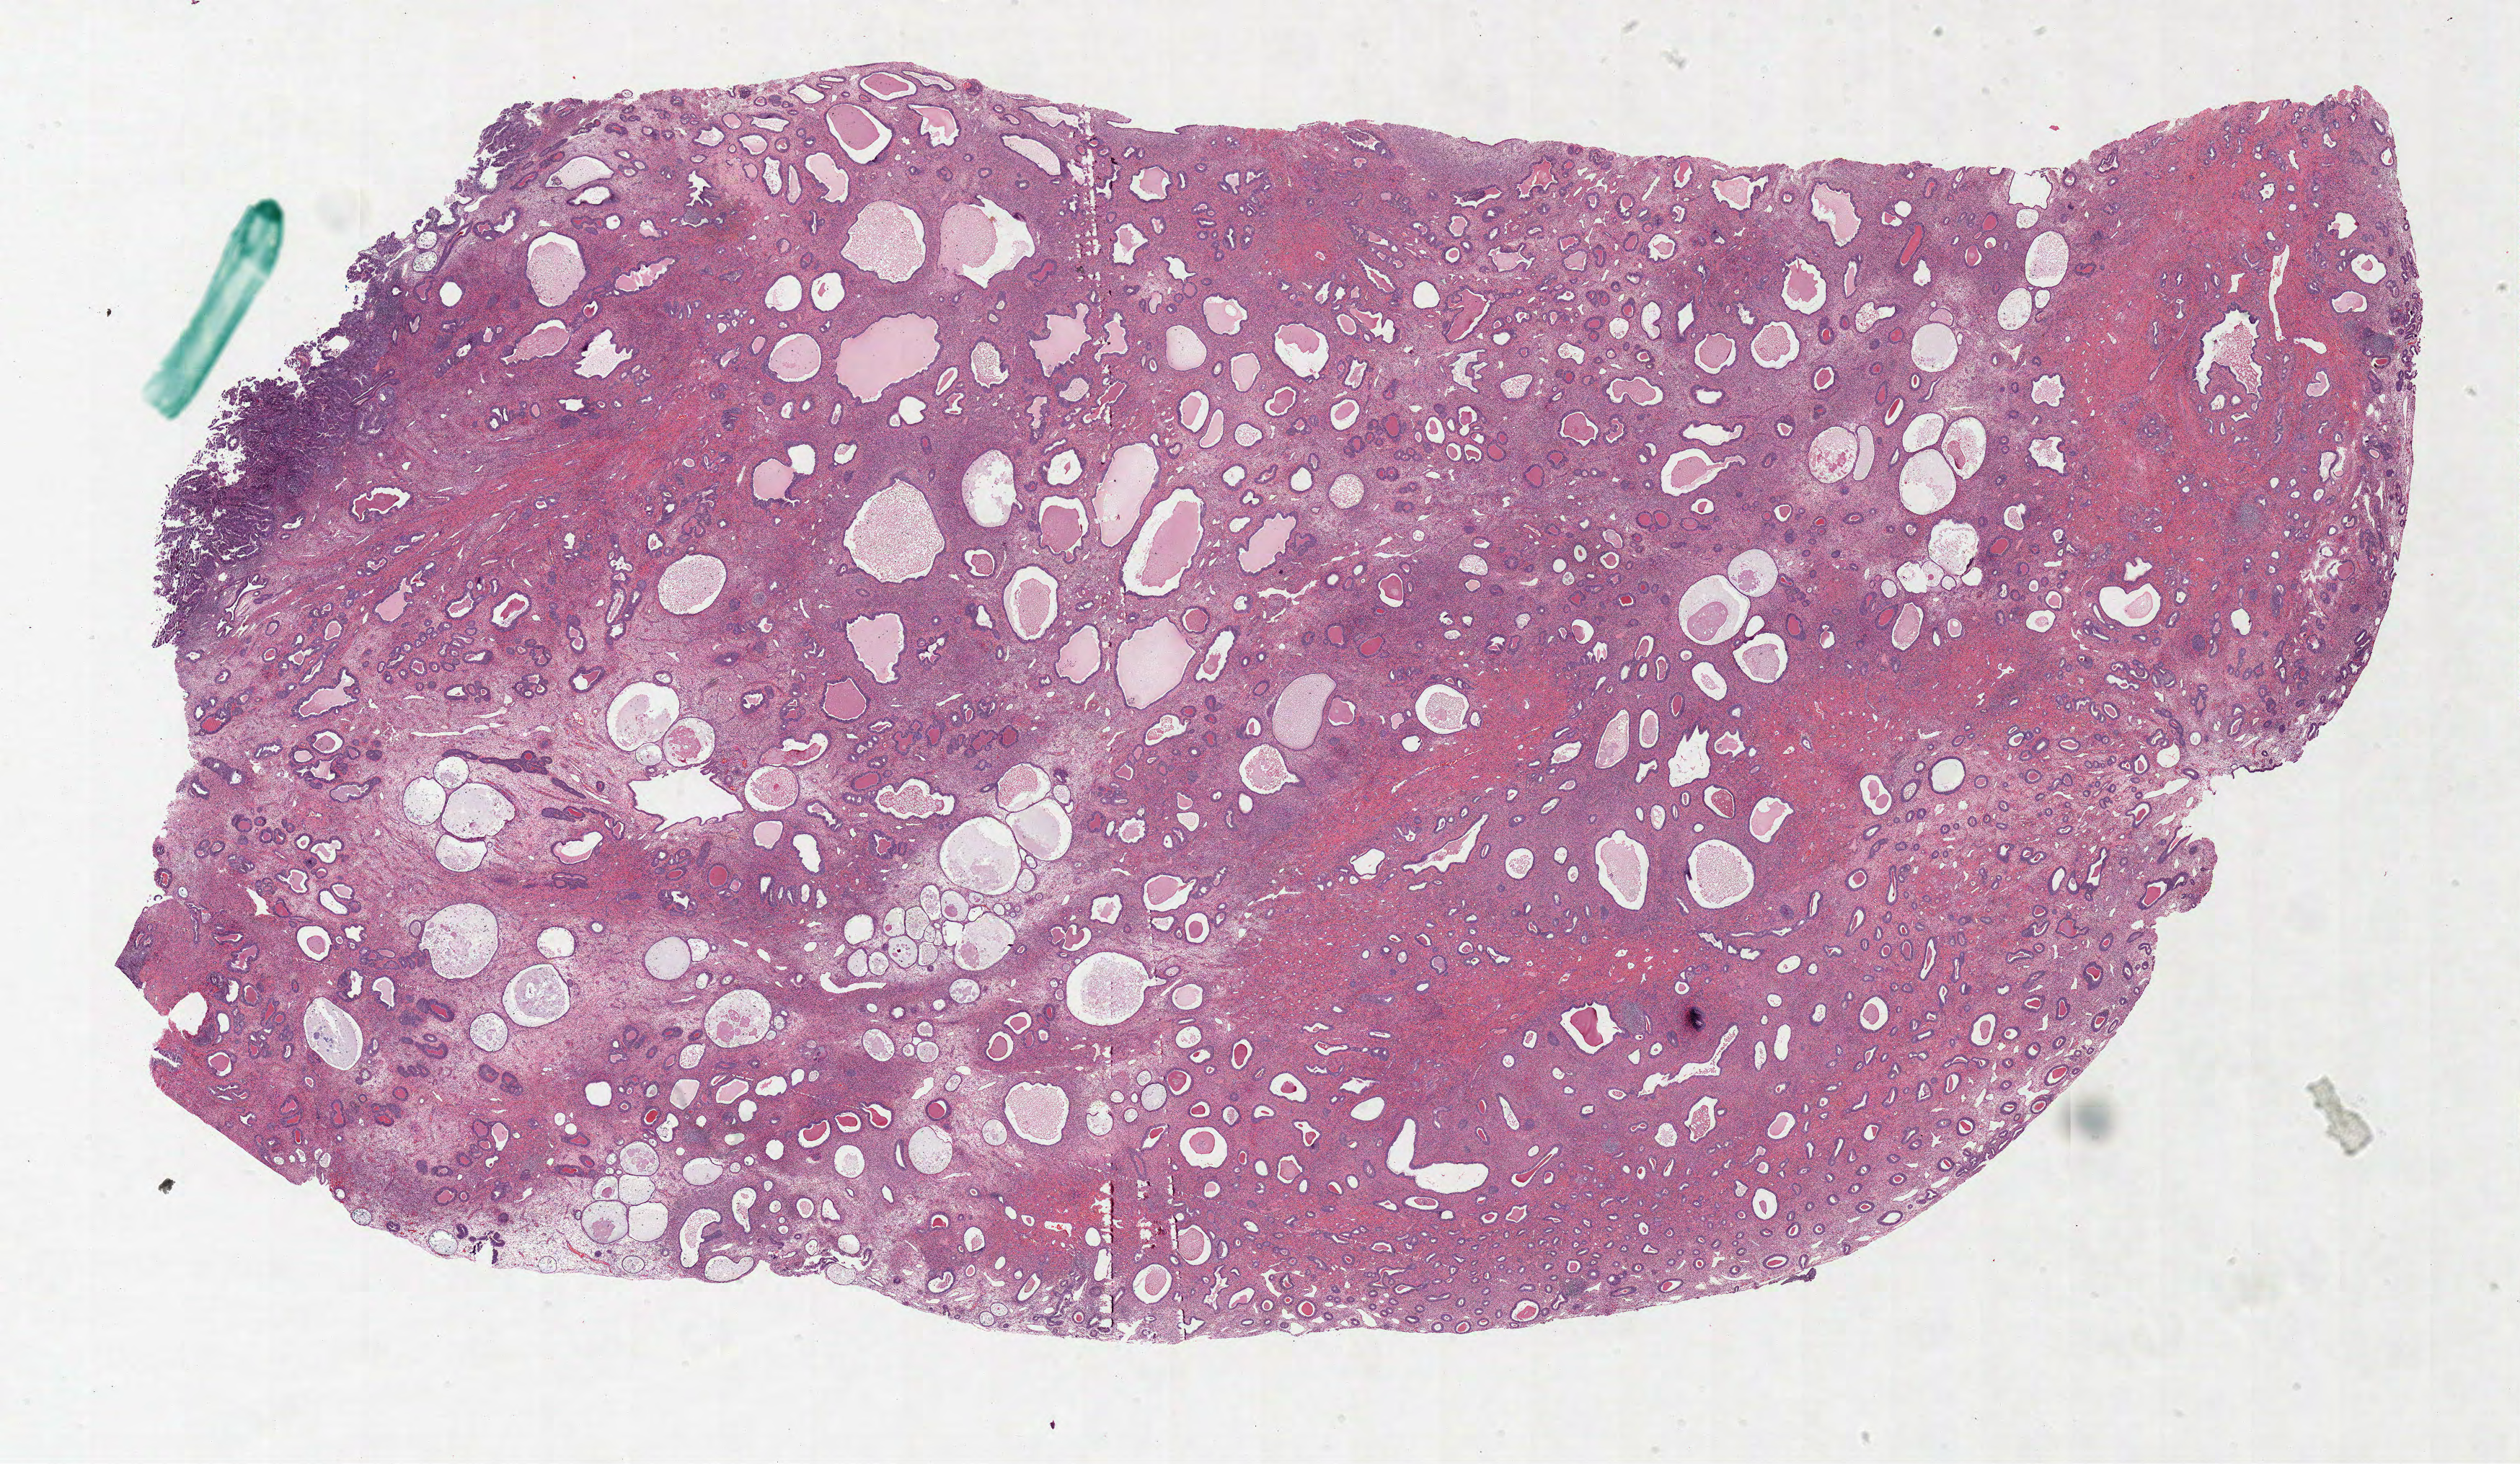
Hematoxylin and eosin (H&E) stained whole-slide image, shown as a low-resolution overview of the whole scanned area (about 27.8 x 16.2 mm). Formalin-fixed paraffin-embedded (FFPE) diagnostic section. Sample: primary tumour, uterus. Female patient; age at initial diagnosis 59 years. Histologic grade: G3 (poorly differentiated).
Histologic diagnosis: Serous cystadenocarcinoma, NOS (endometrium). FIGO stage: IVB.